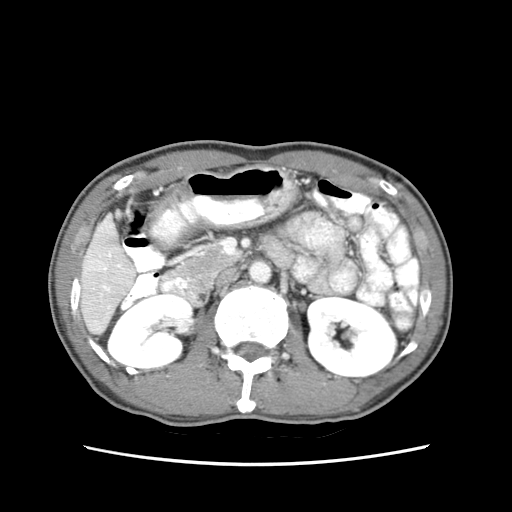
Contrast-enhanced abdominal CT (liver protocol), one axial slice; reconstruction kernel STANDARD; 120 kVp; soft-tissue window (W 400 / L 40 HU); 512 × 512 image matrix, field of view 320 × 320 mm. Case-level facts recorded for this patient, not image findings: diagnosis: hepatocellular carcinoma (patient treated with transarterial chemoembolisation; whether this scan precedes or follows treatment is not stated here); TNM stage (as recorded): Stage-IIIB; Child-Pugh class: A; tumour differentiation: moderately differentiated; tumour nodularity: multinodular.
Outlined on this slice (semi-automatic segmentation, software-assisted and operator-edited):
- liver parenchyma outside the tumour (the mass and vessels are separate outlines, so this box may not span the whole liver): box from (x=80, y=213) to (x=136, y=334) px
- liver vessels: (x=86, y=225)–(x=133, y=321)